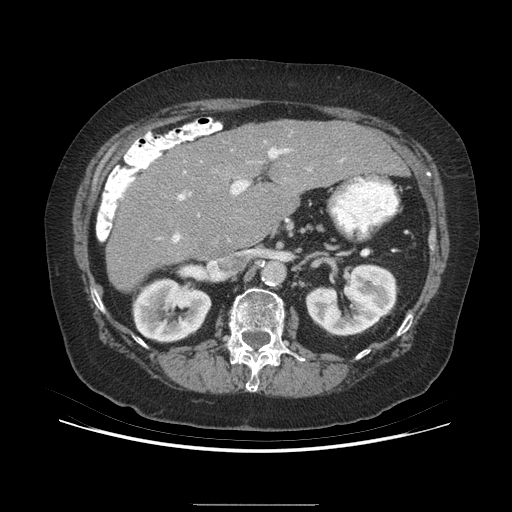
Contrast-enhanced abdominal CT (liver protocol), one axial slice; position 150 of 192 along the scan axis; soft-tissue window (W 400 / L 40 HU); 512 × 512 image matrix, field of view 400 × 400 mm. Case-level facts recorded for this patient, not image findings: diagnosis: hepatocellular carcinoma (patient treated with transarterial chemoembolisation; whether this scan precedes or follows treatment is not stated here); TNM stage (as recorded): Stage-I.
Outlined on this slice (semi-automatic segmentation, software-assisted and operator-edited):
- liver parenchyma outside the tumour (the mass and vessels are separate outlines, so this box may not span the whole liver): bounding box [x1, y1, x2, y2] px = [106, 120, 404, 290]
- liver vessels: [173, 148, 290, 243]